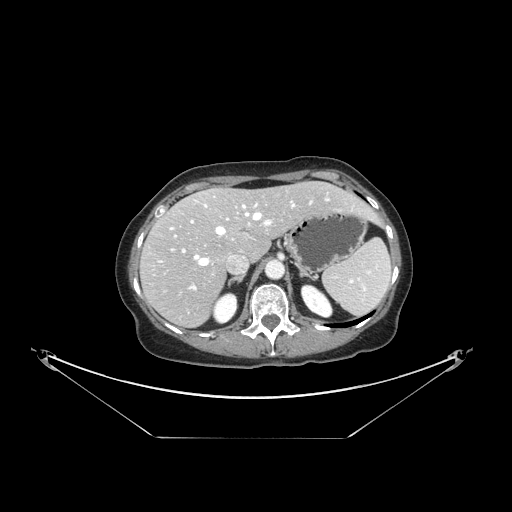
Contrast-enhanced abdominal CT, one axial slice. Slice 103 of 148 in the series (ordered by position). Reconstruction kernel STANDARD. 120 kVp. Intravenous contrast given. Soft-tissue window (W 400 / L 40 HU). 2.5 mm slice thickness. 512 × 512 image matrix. Female patient, age 73 years. Case-level facts recorded for this patient, not image findings: diagnosis: colorectal cancer liver metastases, imaged before liver resection; multiple liver metastases: no; largest metastasis: 1 cm; disease in both lobes: no.
Outlined on this slice (outlined manually by an expert reader):
- hepatic veins: box from (x=170, y=198) to (x=330, y=266) px
- liver: (x=142, y=182)–(x=375, y=326)
- planned liver remnant (the part of the liver to remain after resection): (x=168, y=183)–(x=375, y=259)
- portal vein (with intrahepatic branches): (x=171, y=218)–(x=272, y=290)